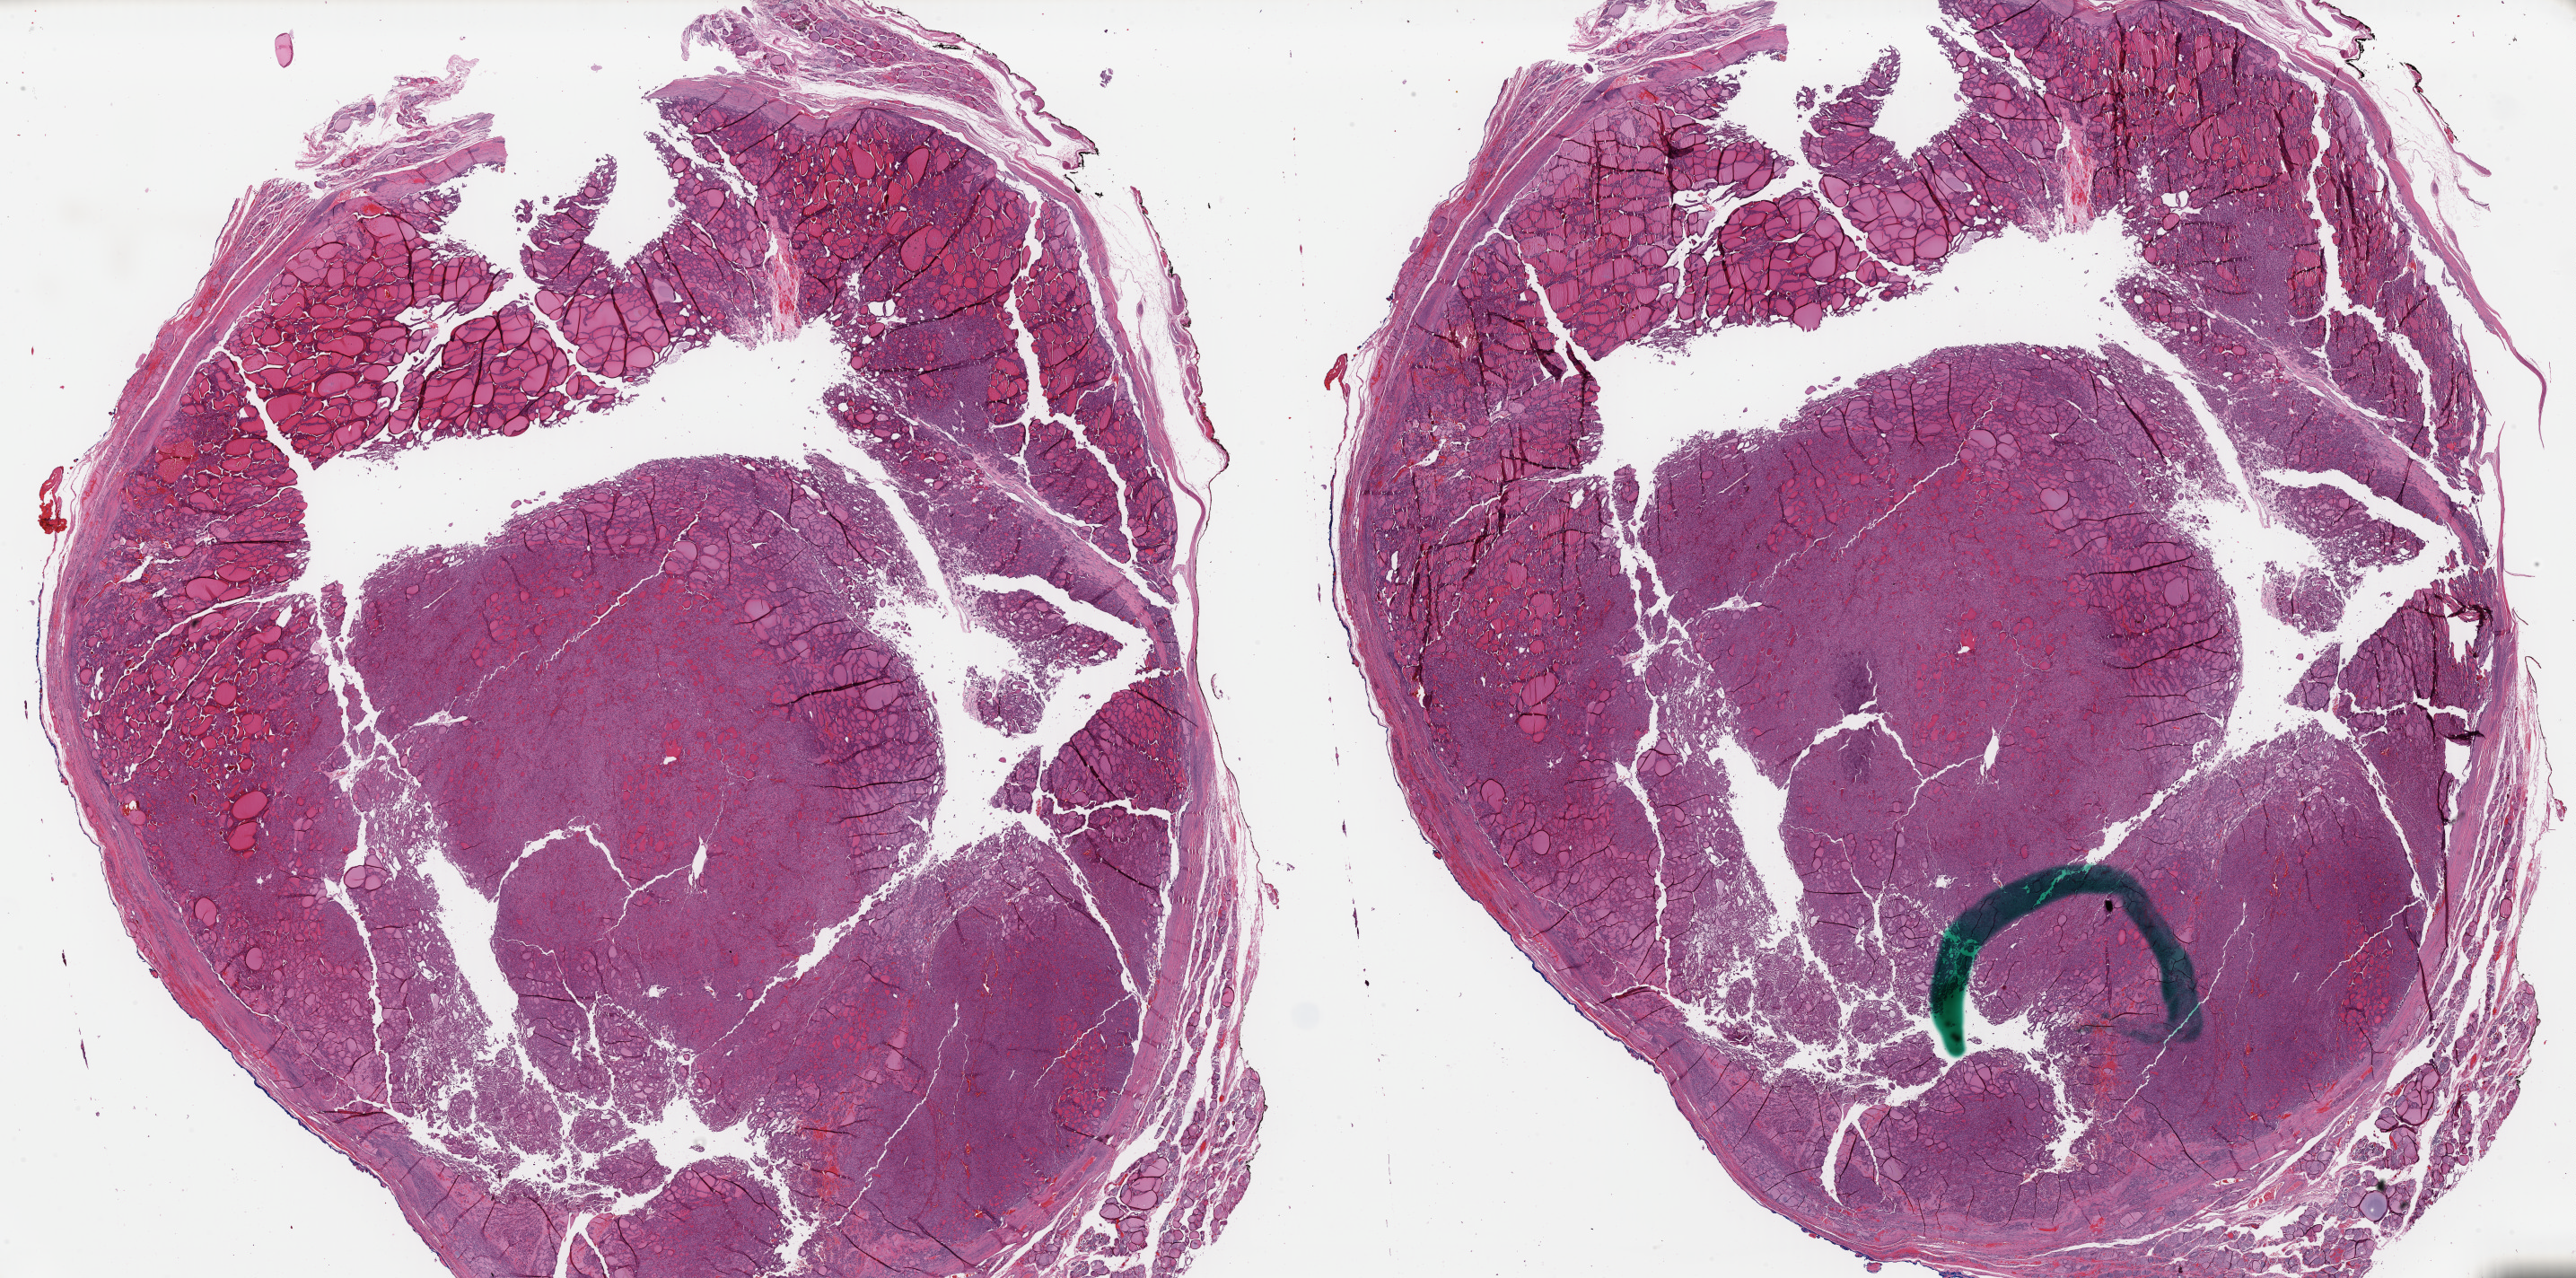
H&E whole-slide image — low-resolution overview of the scanned area, about 45.3 x 22.5 mm, FFPE section, thyroid, primary tumour sample. Patient: female, age at initial diagnosis 68 years.
- AJCC pathologic stage: II
- histologic diagnosis: Papillary carcinoma, follicular variant (thyroid gland)
- laterality: right